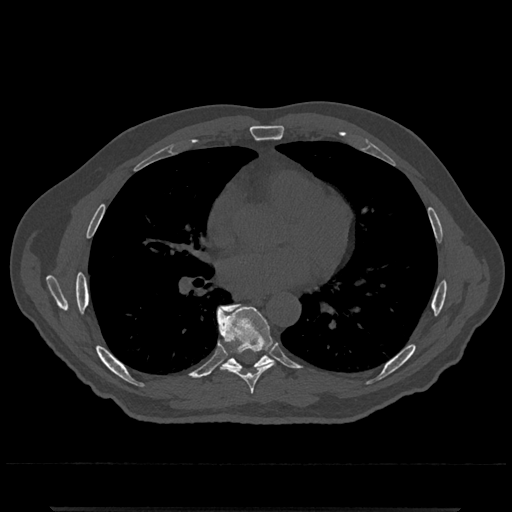
CT including the spine, one axial slice. Position 700 of 797 along the scan axis. 120 kVp. Bone window (W 1800 / L 400 HU). 0.5 mm slice thickness. 512 × 512 image matrix, field of view 393 × 393 mm. Male patient, age 67 years. From the clinical record (not read from this slice): primary cancer: prostate.
Annotated regions visible in this slice (semi-automatically segmented with operator editing):
- T7 vertebra: bounding box [x1, y1, x2, y2] px = [219, 307, 275, 394]
- T8 vertebra: [217, 304, 272, 371]